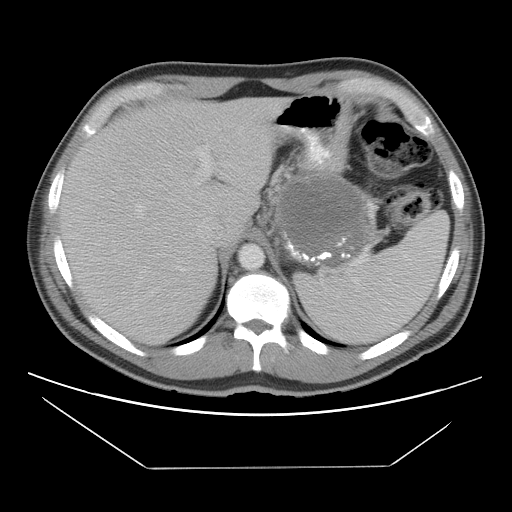
Contrast-enhanced abdominal CT, one axial slice; reconstruction kernel STANDARD; 120 kVp; intravenous contrast given; soft-tissue window (W 400 / L 40 HU); 5 mm slice thickness; 512 × 512 image matrix. Patient: male, 44 years. Case-level facts recorded for this patient, not image findings: diagnosis: adrenocortical carcinoma; tumour side: left adrenal; tumour size at pathology: 15.5 cm; Ki-67 index: 6 %.
Structures marked on this image (semi-automatically segmented with operator editing):
- mass: bounding box (x1, y1, x2, y2) in pixels: (278, 175, 367, 267)